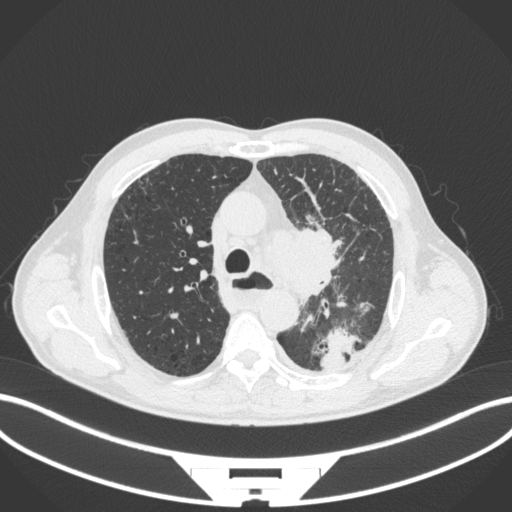
Chest CT, one axial slice; slice 268 of 411 in the series (ordered by position); reconstruction kernel B31f; 120 kVp; lung window (W 1500 / L -600 HU); 1 mm slice thickness; 512 × 512 image matrix, field of view 400 × 400 mm. Male patient, age 57 years. From the clinical record (not read from this slice): clinical TNM (as recorded): T2a N1 M0.
Structures marked on this image (rectangle marked by the reading radiologist):
- lung tumour (recorded histology: squamous cell carcinoma): box from (x=265, y=221) to (x=350, y=308) px